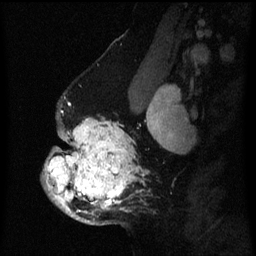
Breast MRI (dynamic contrast-enhanced), one sagittal slice; position 43 of 60 along the scan axis; dynamic contrast-enhanced series, image 2 of 3 at this slice position (ordered by acquisition); 1.5 T; TE 4.2 ms, TR 8 ms; 256 × 256 image matrix, field of view 190 × 190 mm. Patient: female, 50 years.
Structures marked on this image (semi-automatically segmented with operator editing):
- analysis volume of interest (the breast-tissue region the enhancement analysis was run in; not a lesion): bounding box [x1, y1, x2, y2] px = [41, 113, 139, 225]
- tumour enhancement mask (voxels above the 70 % enhancement threshold inside the analysis volume of interest): [44, 119, 138, 222]